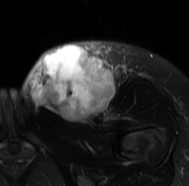
MRI of an extremity soft-tissue mass, one axial slice; position 38 of 77 along the scan axis; T2-weighted fat-saturated; MR volume resampled by the dataset authors to the PET/CT grid (not the native acquisition matrix); 3.27 mm slice thickness; 189 × 186 image matrix, field of view 185 × 182 mm. Female patient. Case-level facts recorded for this patient, not image findings: histological type: leiomyosarcoma; grade: high; site of the primary tumour: groin.
Annotated regions visible in this slice (expert contour drawn on MRI and transferred to this co-registered scan by the dataset authors):
- gross tumour volume including surrounding oedema: box from (x=22, y=40) to (x=132, y=124) px
- gross tumour volume (mass): (x=31, y=45)–(x=114, y=121)